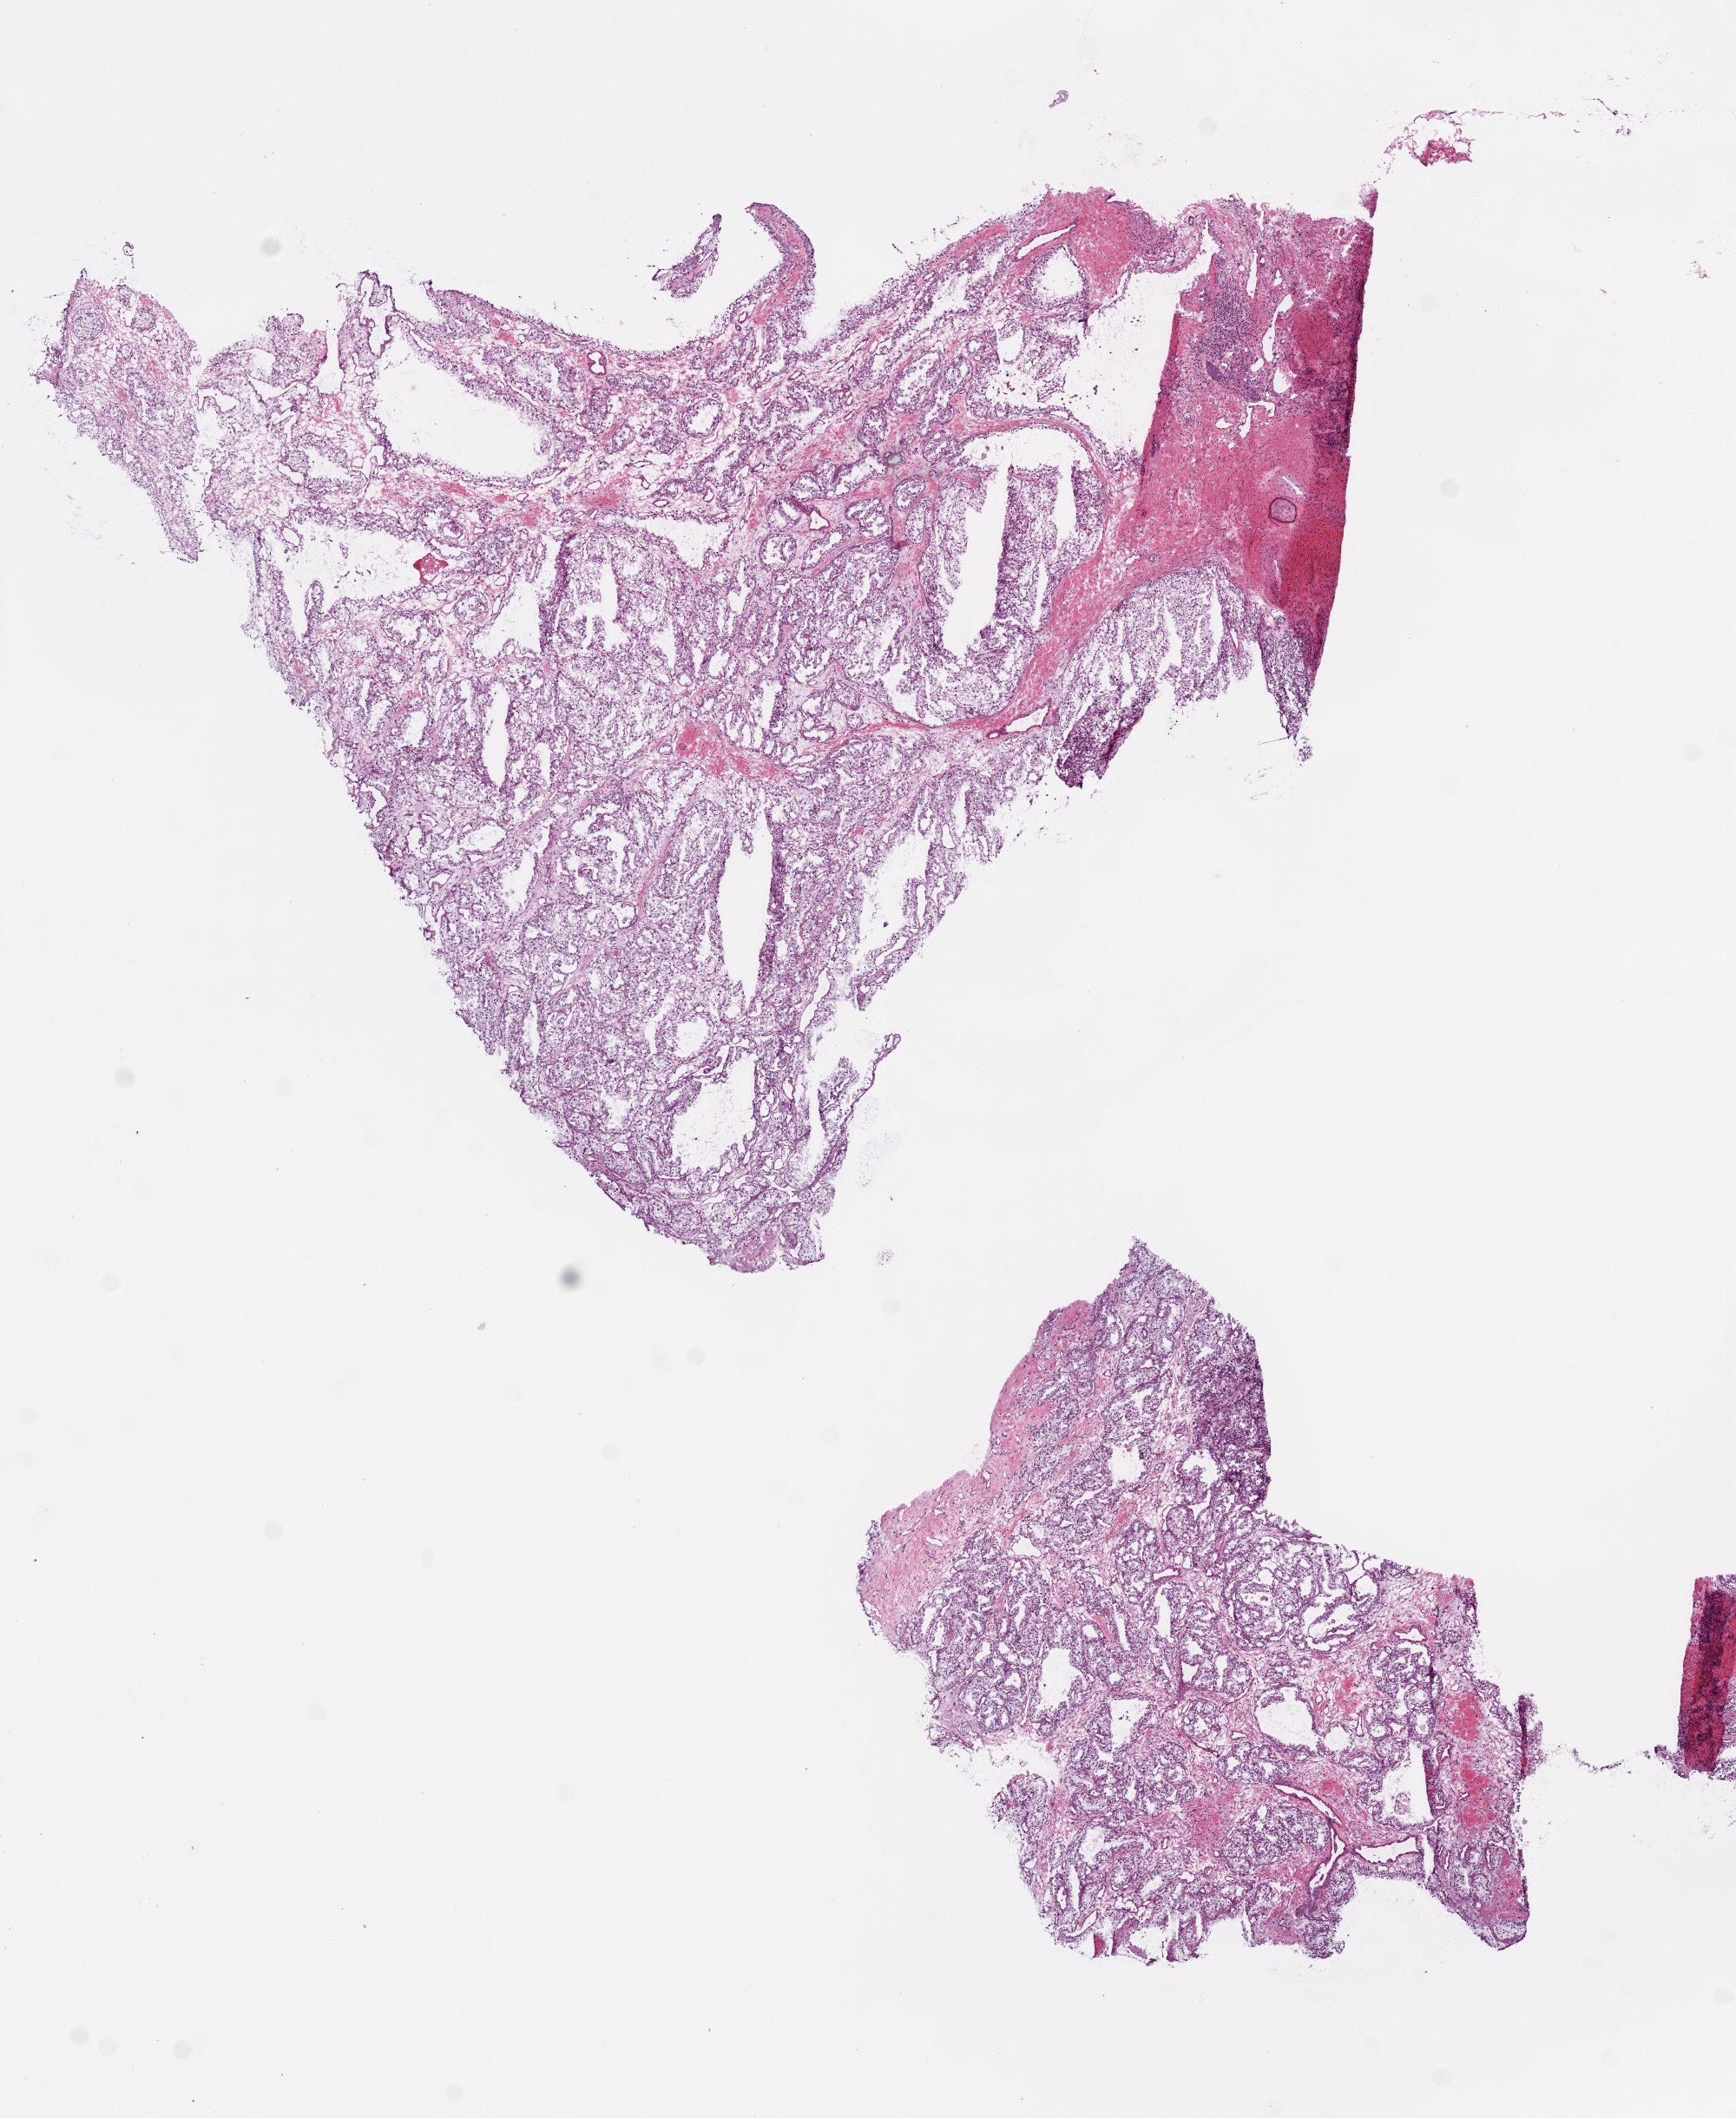
Digitized Hematoxylin and eosin (H&E) stained tissue section (whole slide) — whole scanned area (about 8.0 x 9.8 mm, acquisition: 20x scan) shown as a low-resolution overview; frozen section; primary tumour sample from the kidney. Female, age 74 years at initial diagnosis. Histologic grade: G2 (moderately differentiated). Composition of this section per pathologist review: tumour cells 95%, tumour nuclei 80%, normal cells 0%, stromal cells 5%, necrosis 0%.
• AJCC pathologic stage: I
• pathologic diagnosis: Clear cell adenocarcinoma, NOS